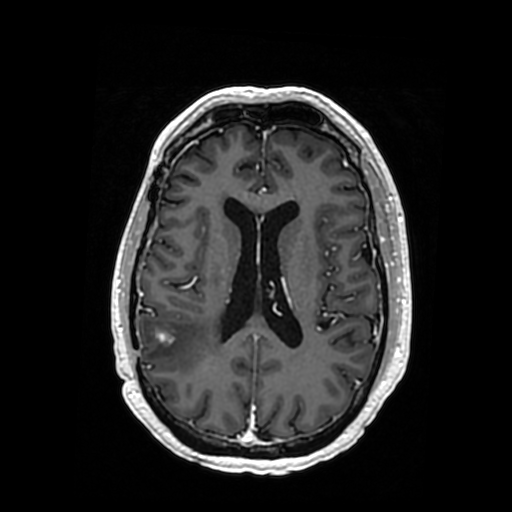
Brain MRI from a brain-tumour surgery series, one axial slice. Slice 154 of 364 in the series (ordered by position). T1-weighted post-contrast. 0.5 mm slice thickness. 512 × 512 image matrix, field of view 260 × 260 mm. Case-level facts recorded for this patient, not image findings: histopathology: Oligodendroglioma; WHO grade: 3; IDH mutation: yes; tumour location: Right Posterior Temporal Inferior Parietal.
Annotated regions visible in this slice (expert manual segmentation):
- tumour: box from (x=178, y=326) to (x=198, y=343) px